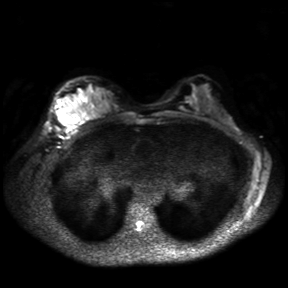
Breast MRI, one axial slice; slice 20 of 30 in the series (ordered by position); diffusion-weighted series; image 2 of 4 stored at this slice position (different b-values; order by instance number); 3 T; 4 mm slice thickness; 288 × 288 image matrix, field of view 360 × 360 mm. Female patient.
Annotated regions visible in this slice (outlined manually by an expert reader):
- tumour on diffusion-weighted imaging: bounding box <57,101,77,125> (left, top, right, bottom; pixels)